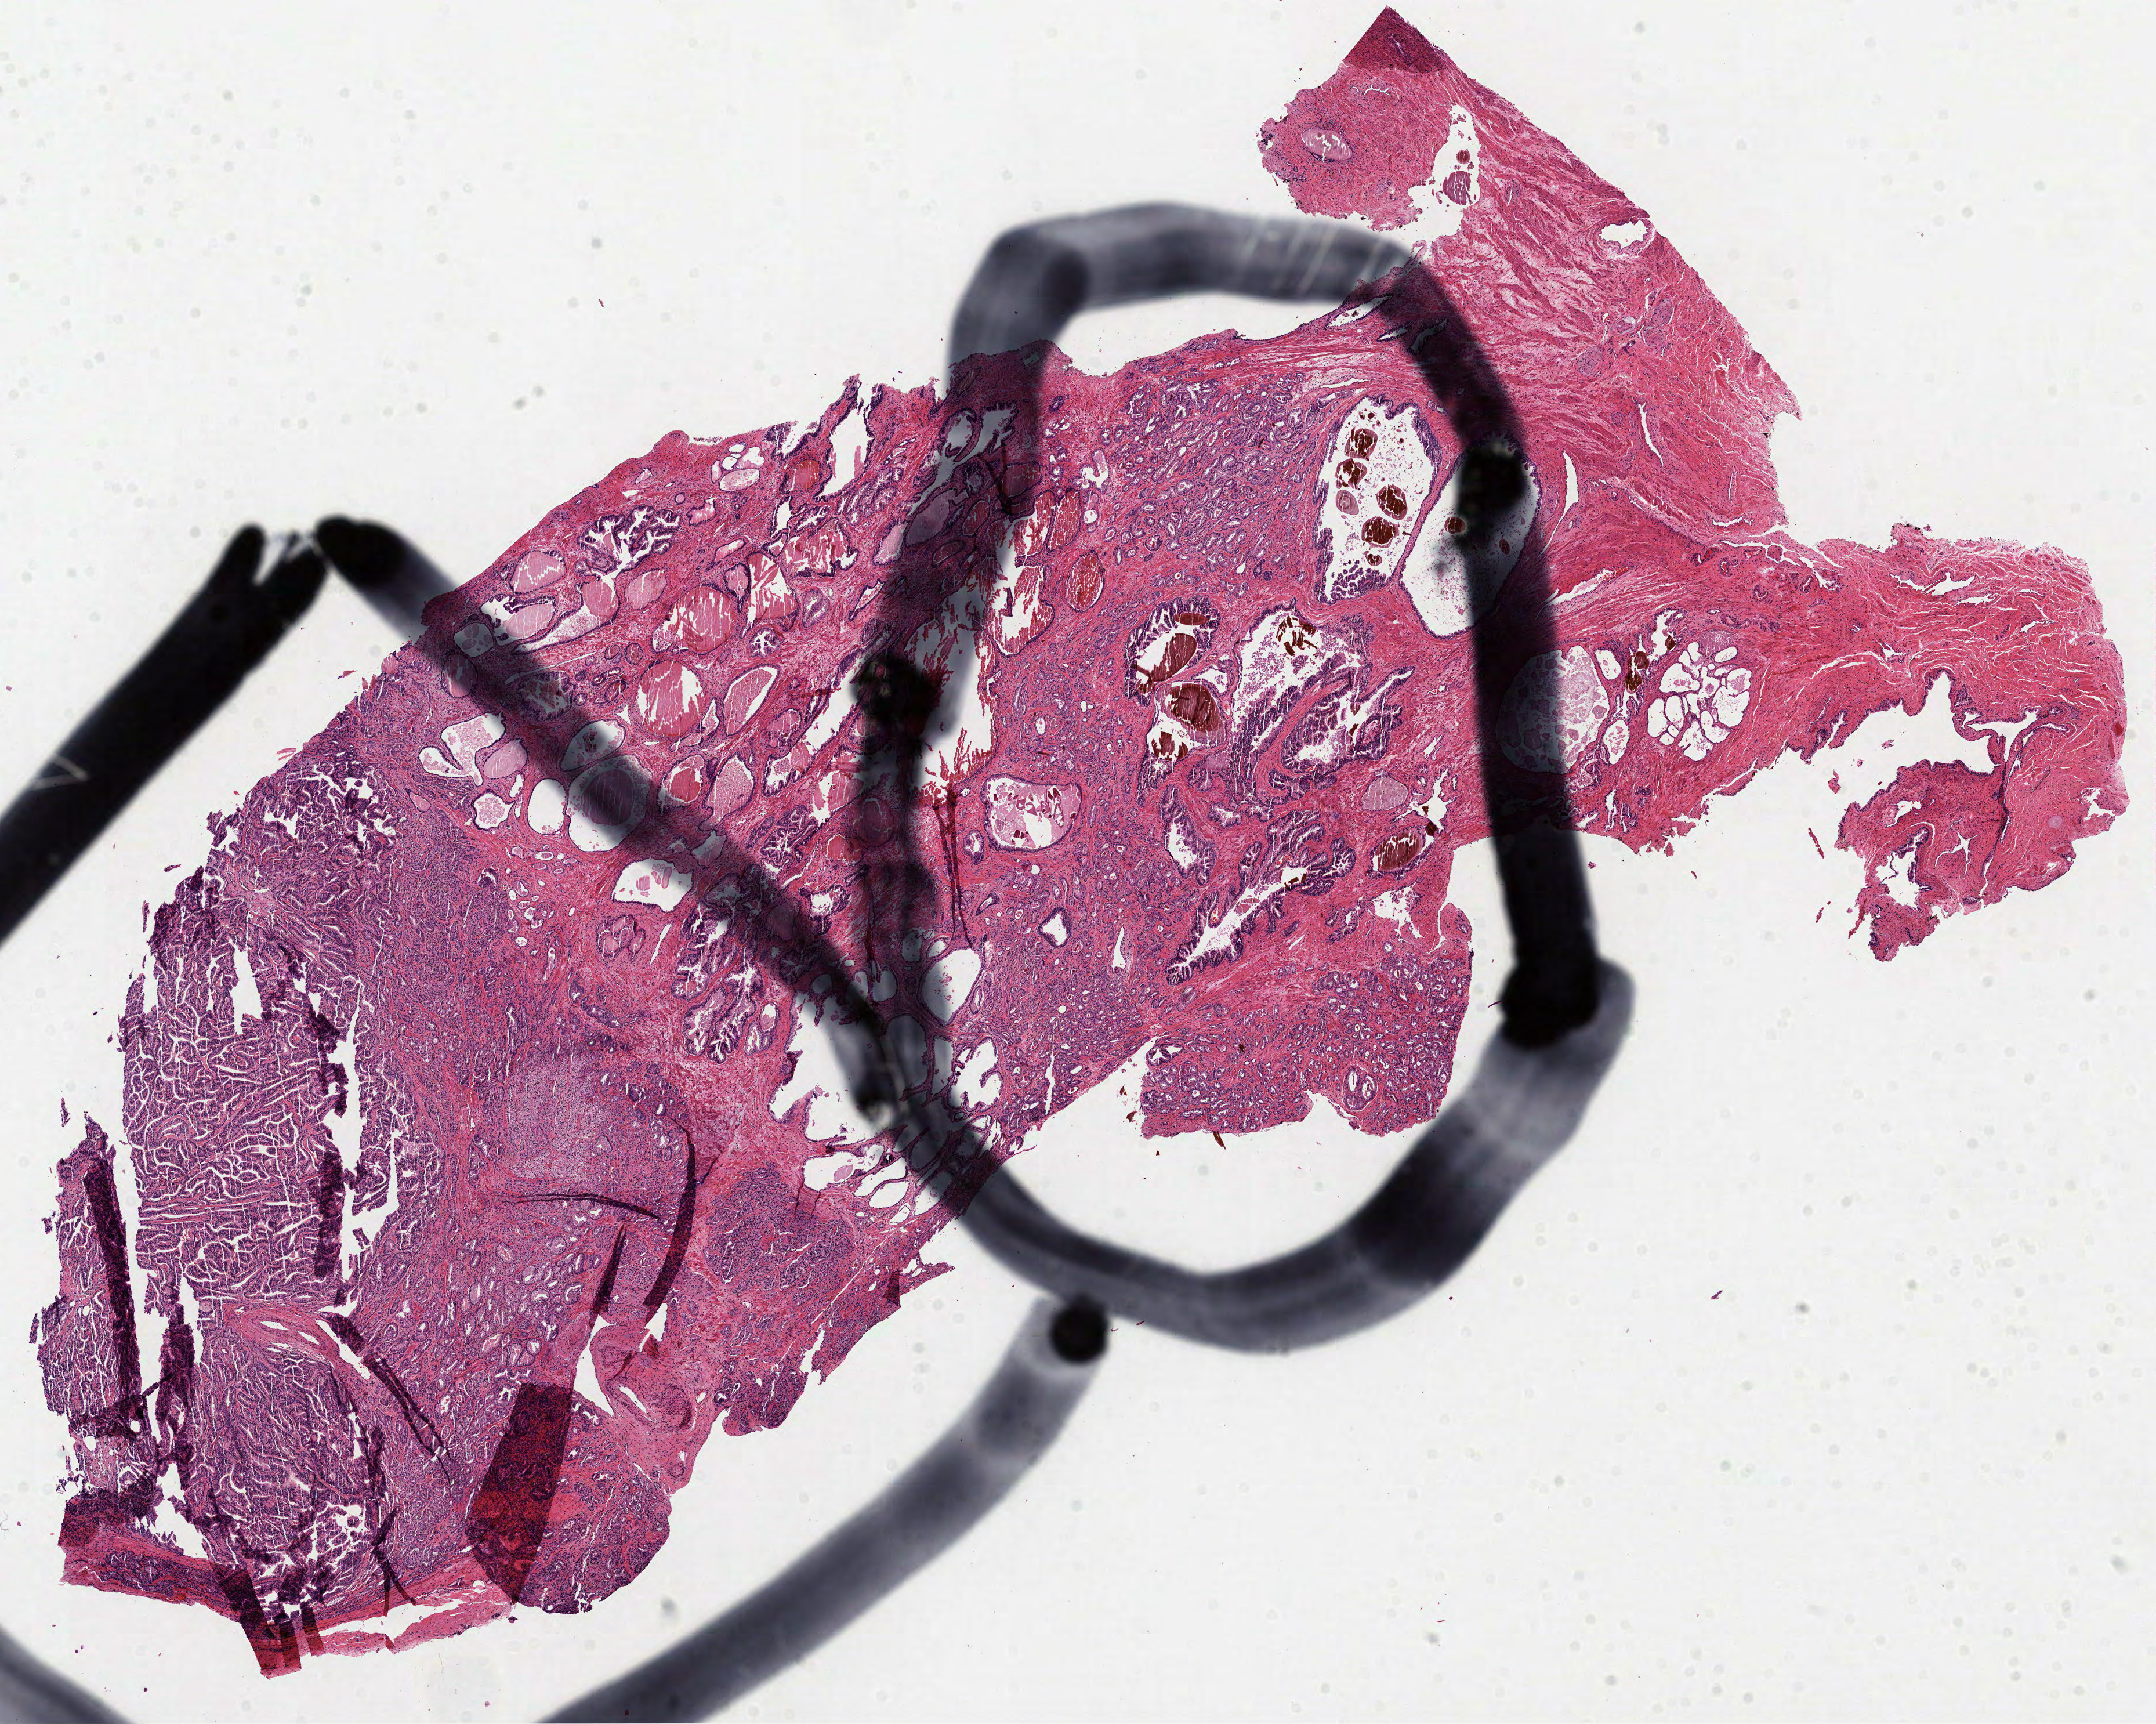
H&E whole-slide image, a low-resolution overview of the entire scanned area, about 15.0 x 12.0 mm (slide scanned at 40x); formalin-fixed paraffin-embedded (FFPE) diagnostic section; sample: primary tumour, prostate. Male, age 62 years at initial diagnosis. Gleason score: 7 (4+3).
* pathologic diagnosis: Acinar cell carcinoma (prostate gland)
* laterality: bilateral